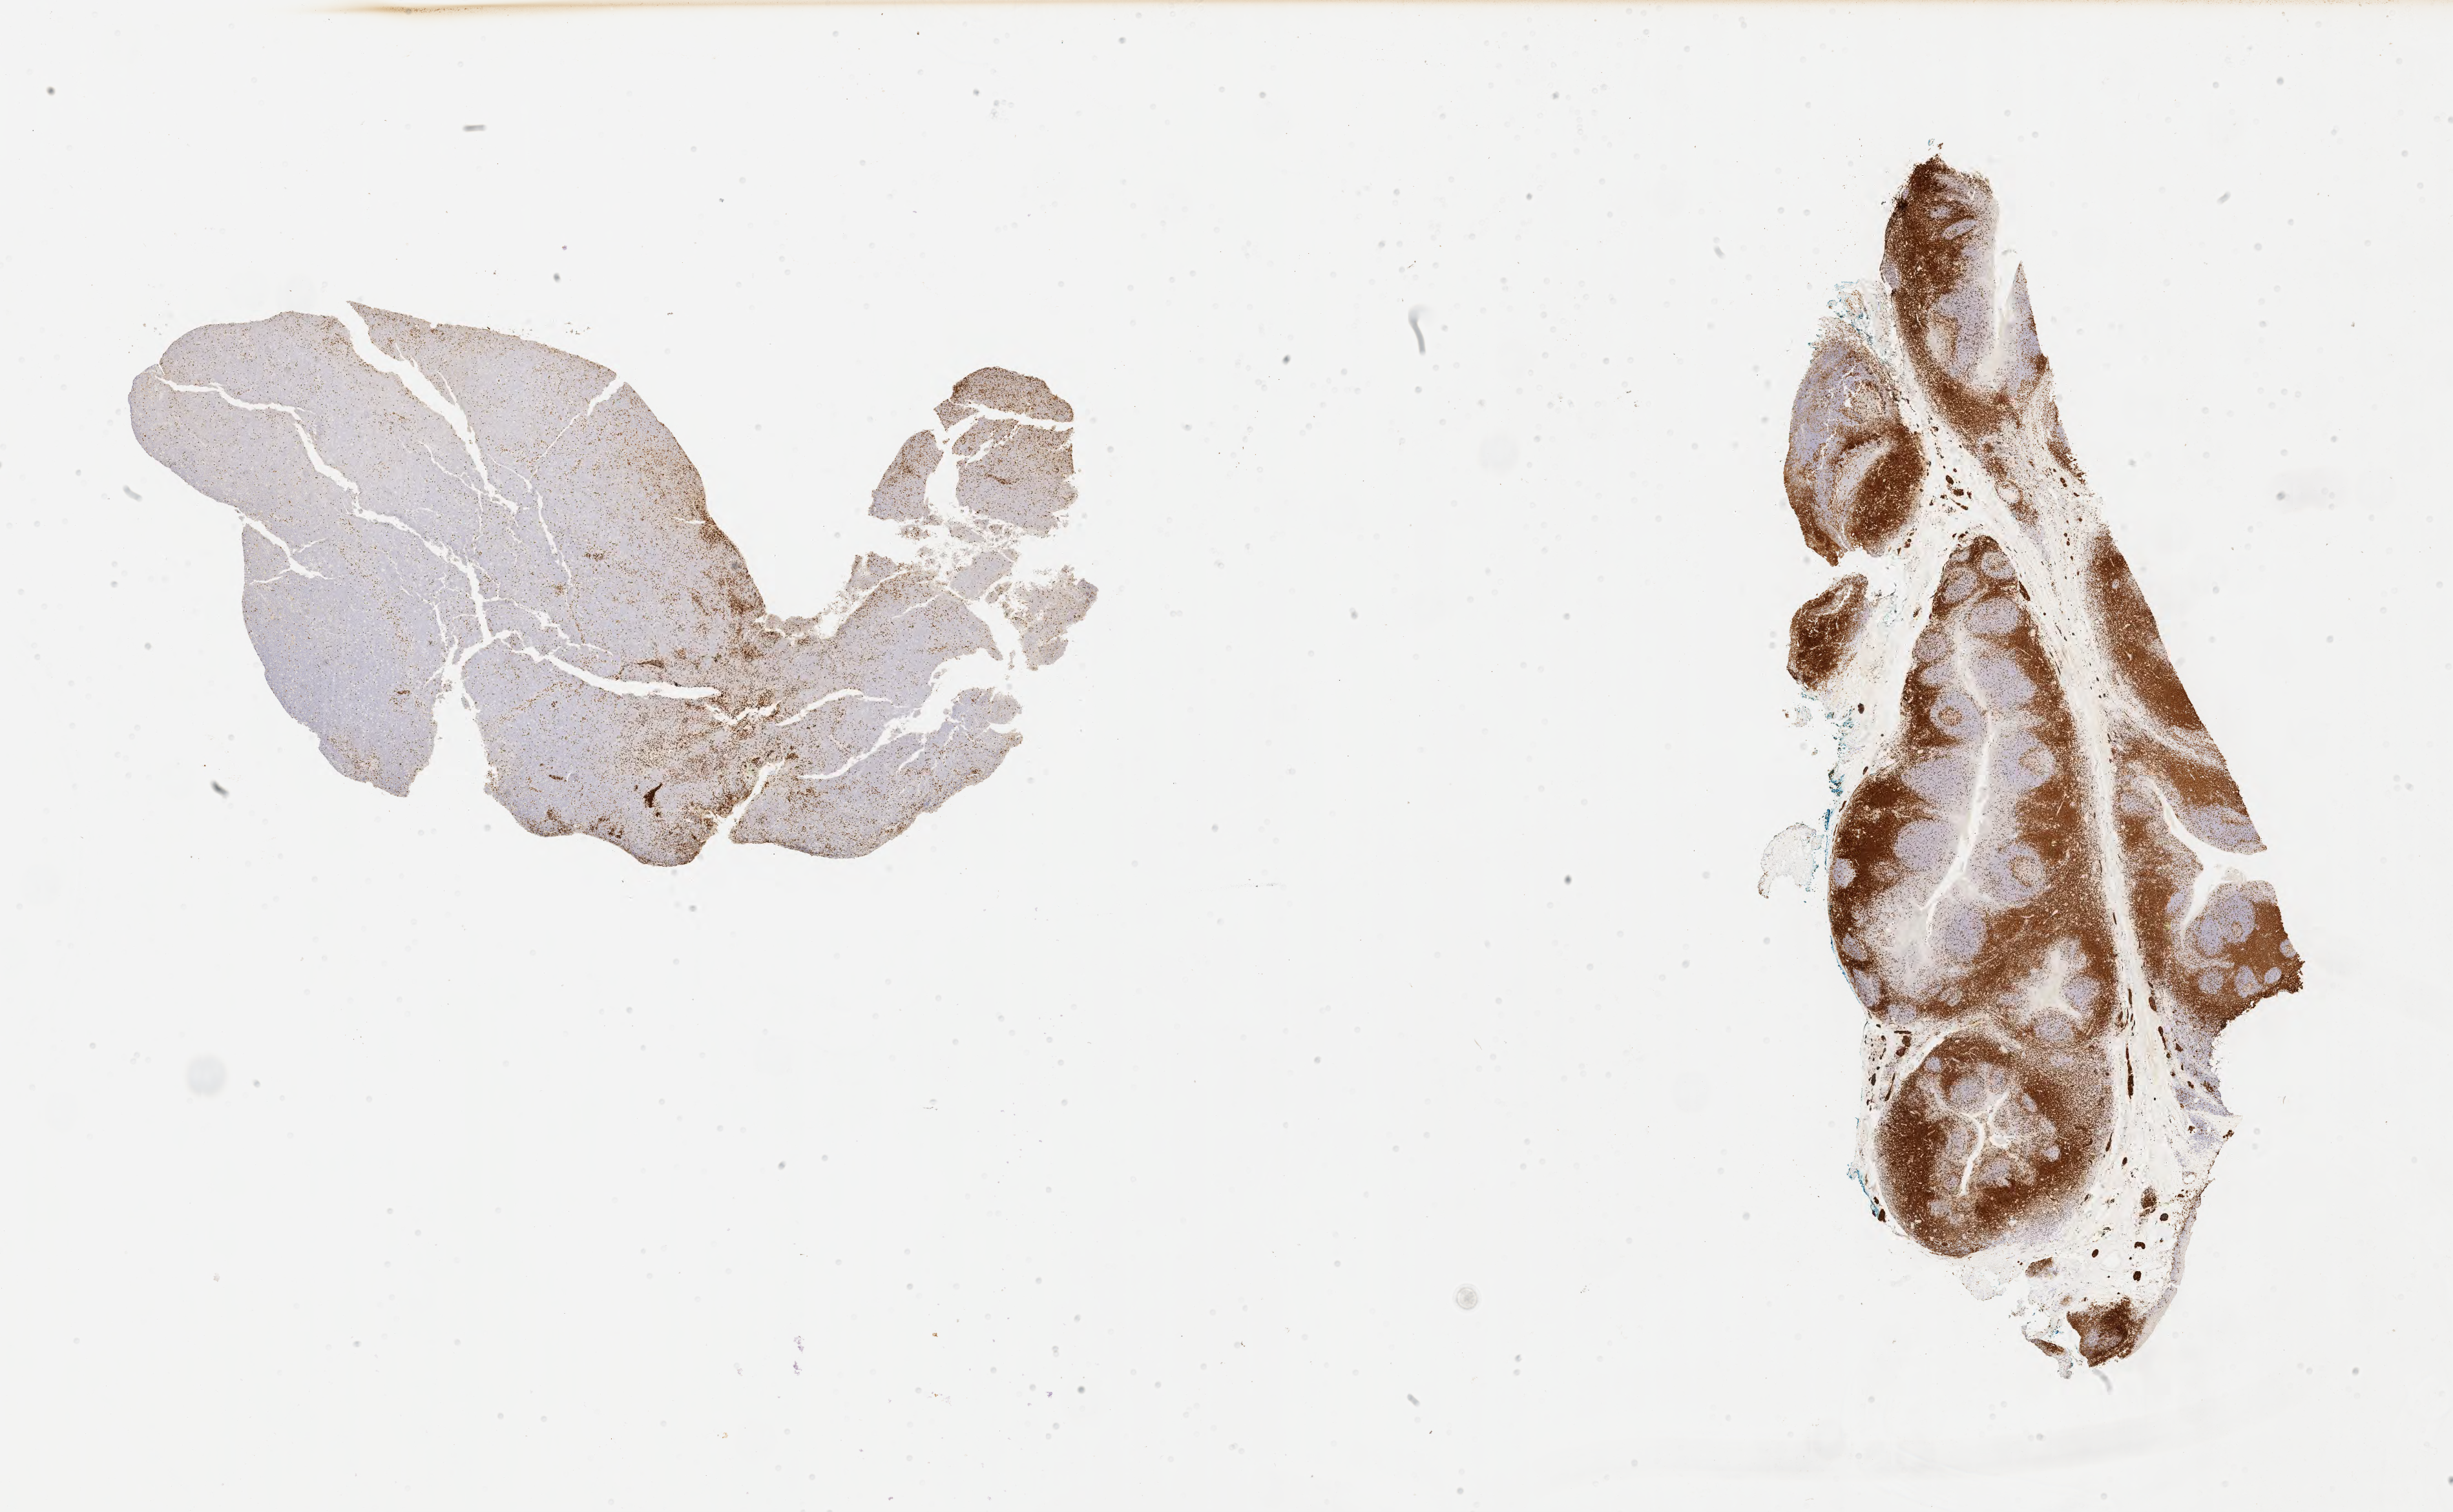
IHC for CD3, whole-slide image, low-resolution overview of the scanned area, about 30.7 x 18.9 mm; tumor tissue; anatomic site: lymph node of head and neck. Male, age 5 years at initial diagnosis.
Diagnosis: Burkitt lymphoma, NOS.